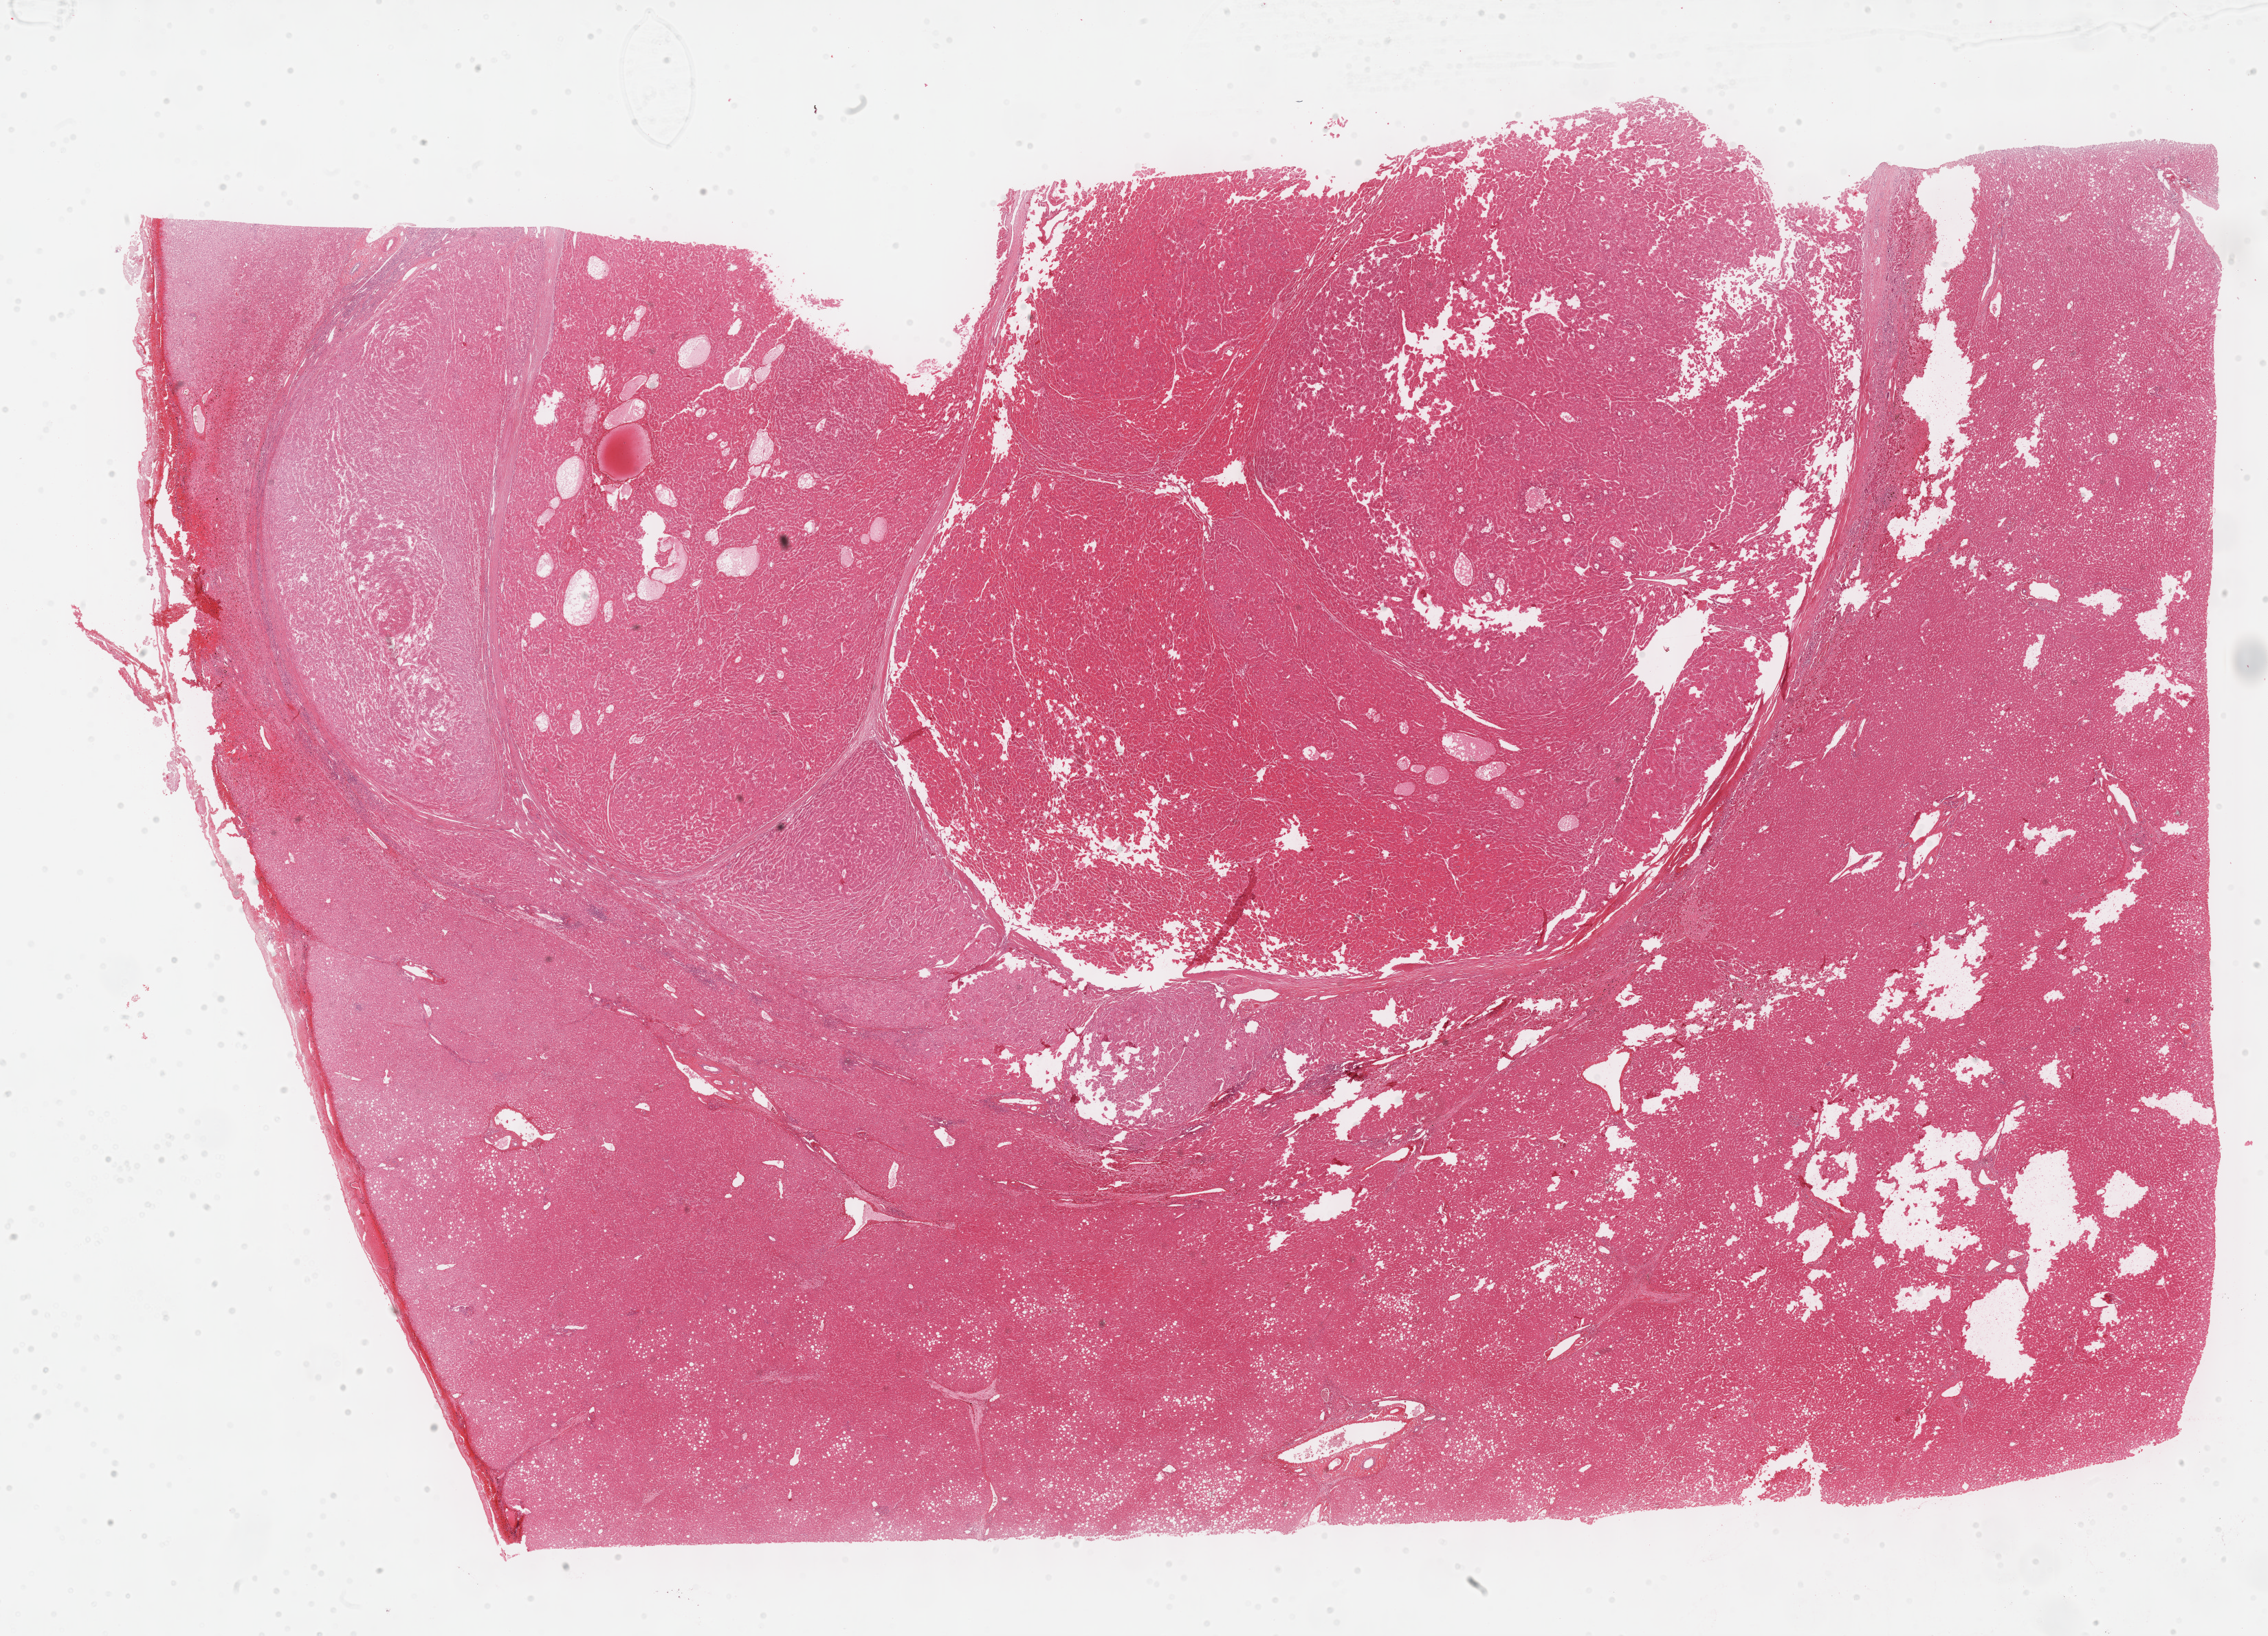
H&E-stained whole-slide image, a low-resolution overview of the entire scanned area, about 26.7 x 19.2 mm. FFPE section. Sample: primary tumour, liver. Male patient; age at initial diagnosis 53 years. Histologic grade: G2 (moderately differentiated).
Diagnosis: Hepatocellular carcinoma, NOS. AJCC pathologic stage: II (7th edition).